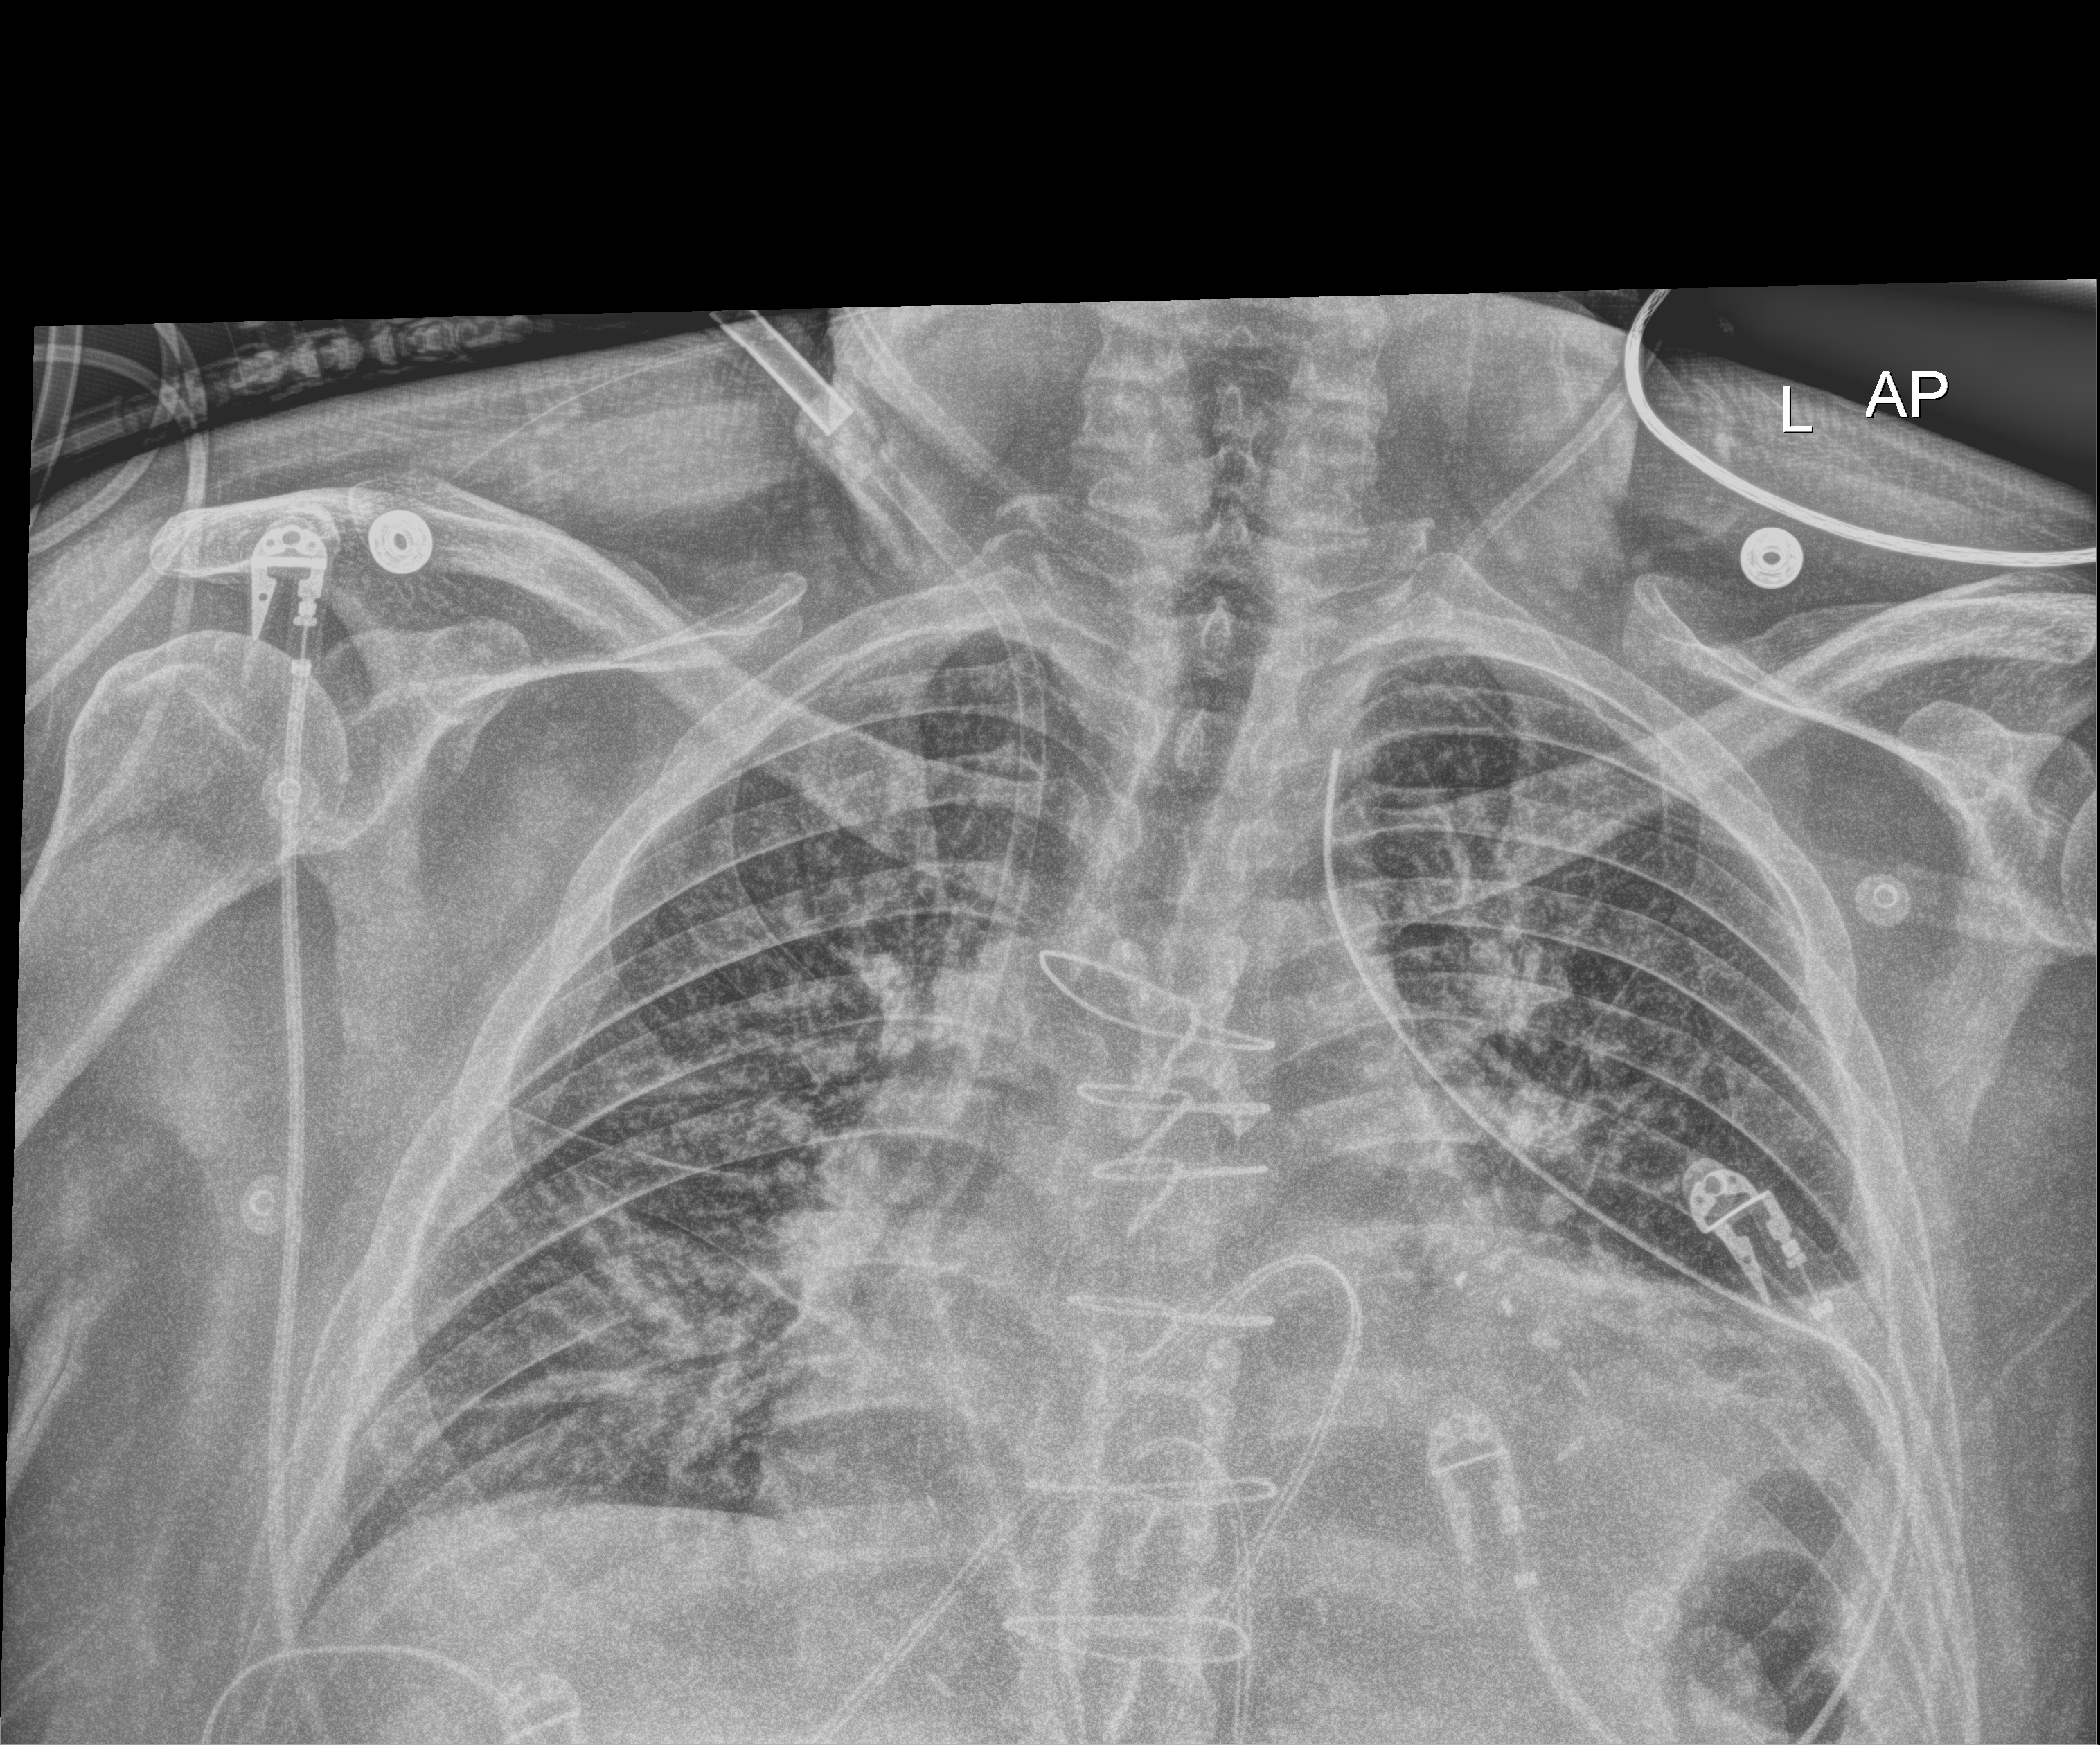
Bedside chest radiograph (digital radiography), anteroposterior (AP) projection. Patient hospitalised with COVID-19; male, aged 18–59 years.
From the hospital-stay record, not from the radiograph (when in the stay this image was taken is not recorded): mechanically ventilated during this hospital stay: no; admitted to intensive care during this hospital stay: no.